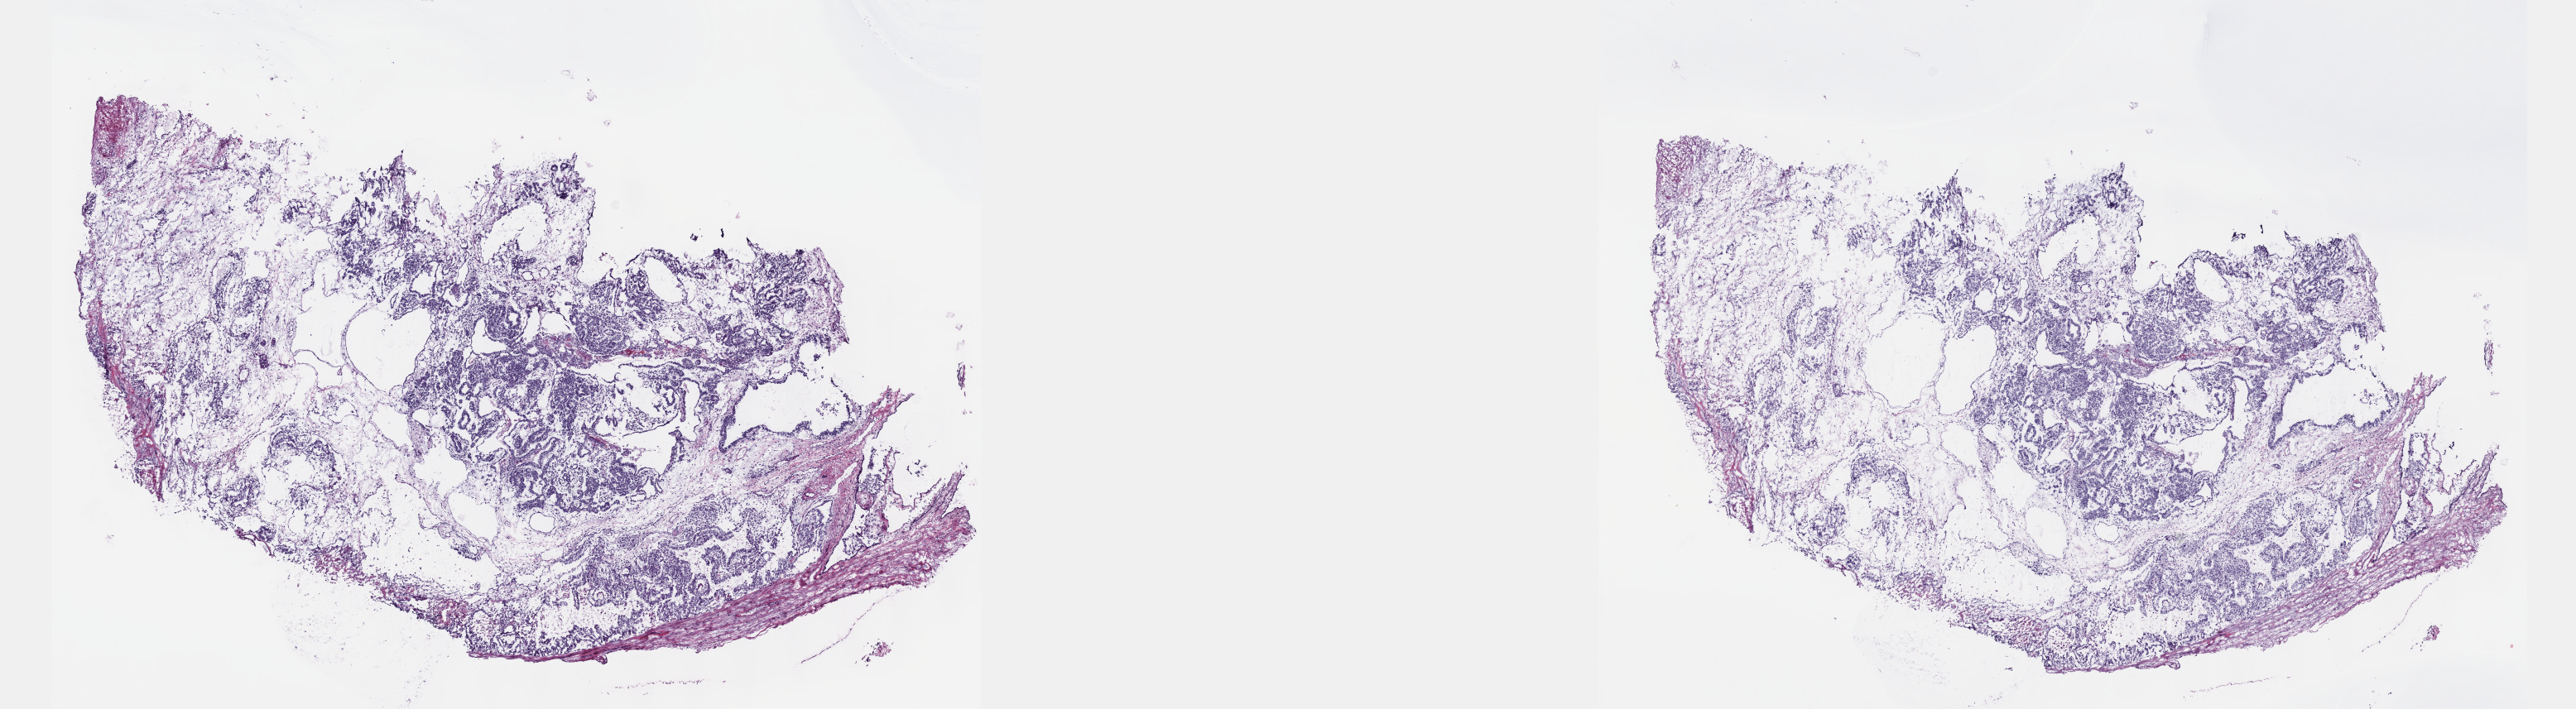
H&E whole-slide image — shown as a low-resolution overview of the whole scanned area (about 25.1 x 6.9 mm, acquisition: 40x scan), frozen section, testis, primary tumour sample. Male, age 51 years at initial diagnosis. Slide review estimates, as recorded: tumour cells 70%, tumour nuclei 70%, normal cells 0%, stromal cells 10%, necrosis 20%. Inflammatory infiltration, as recorded: lymphocyte infiltration 40%, monocyte infiltration 20%, neutrophil infiltration 20%.
Diagnosis: Yolk sac tumor. AJCC pathologic stage: IS. Laterality: right.